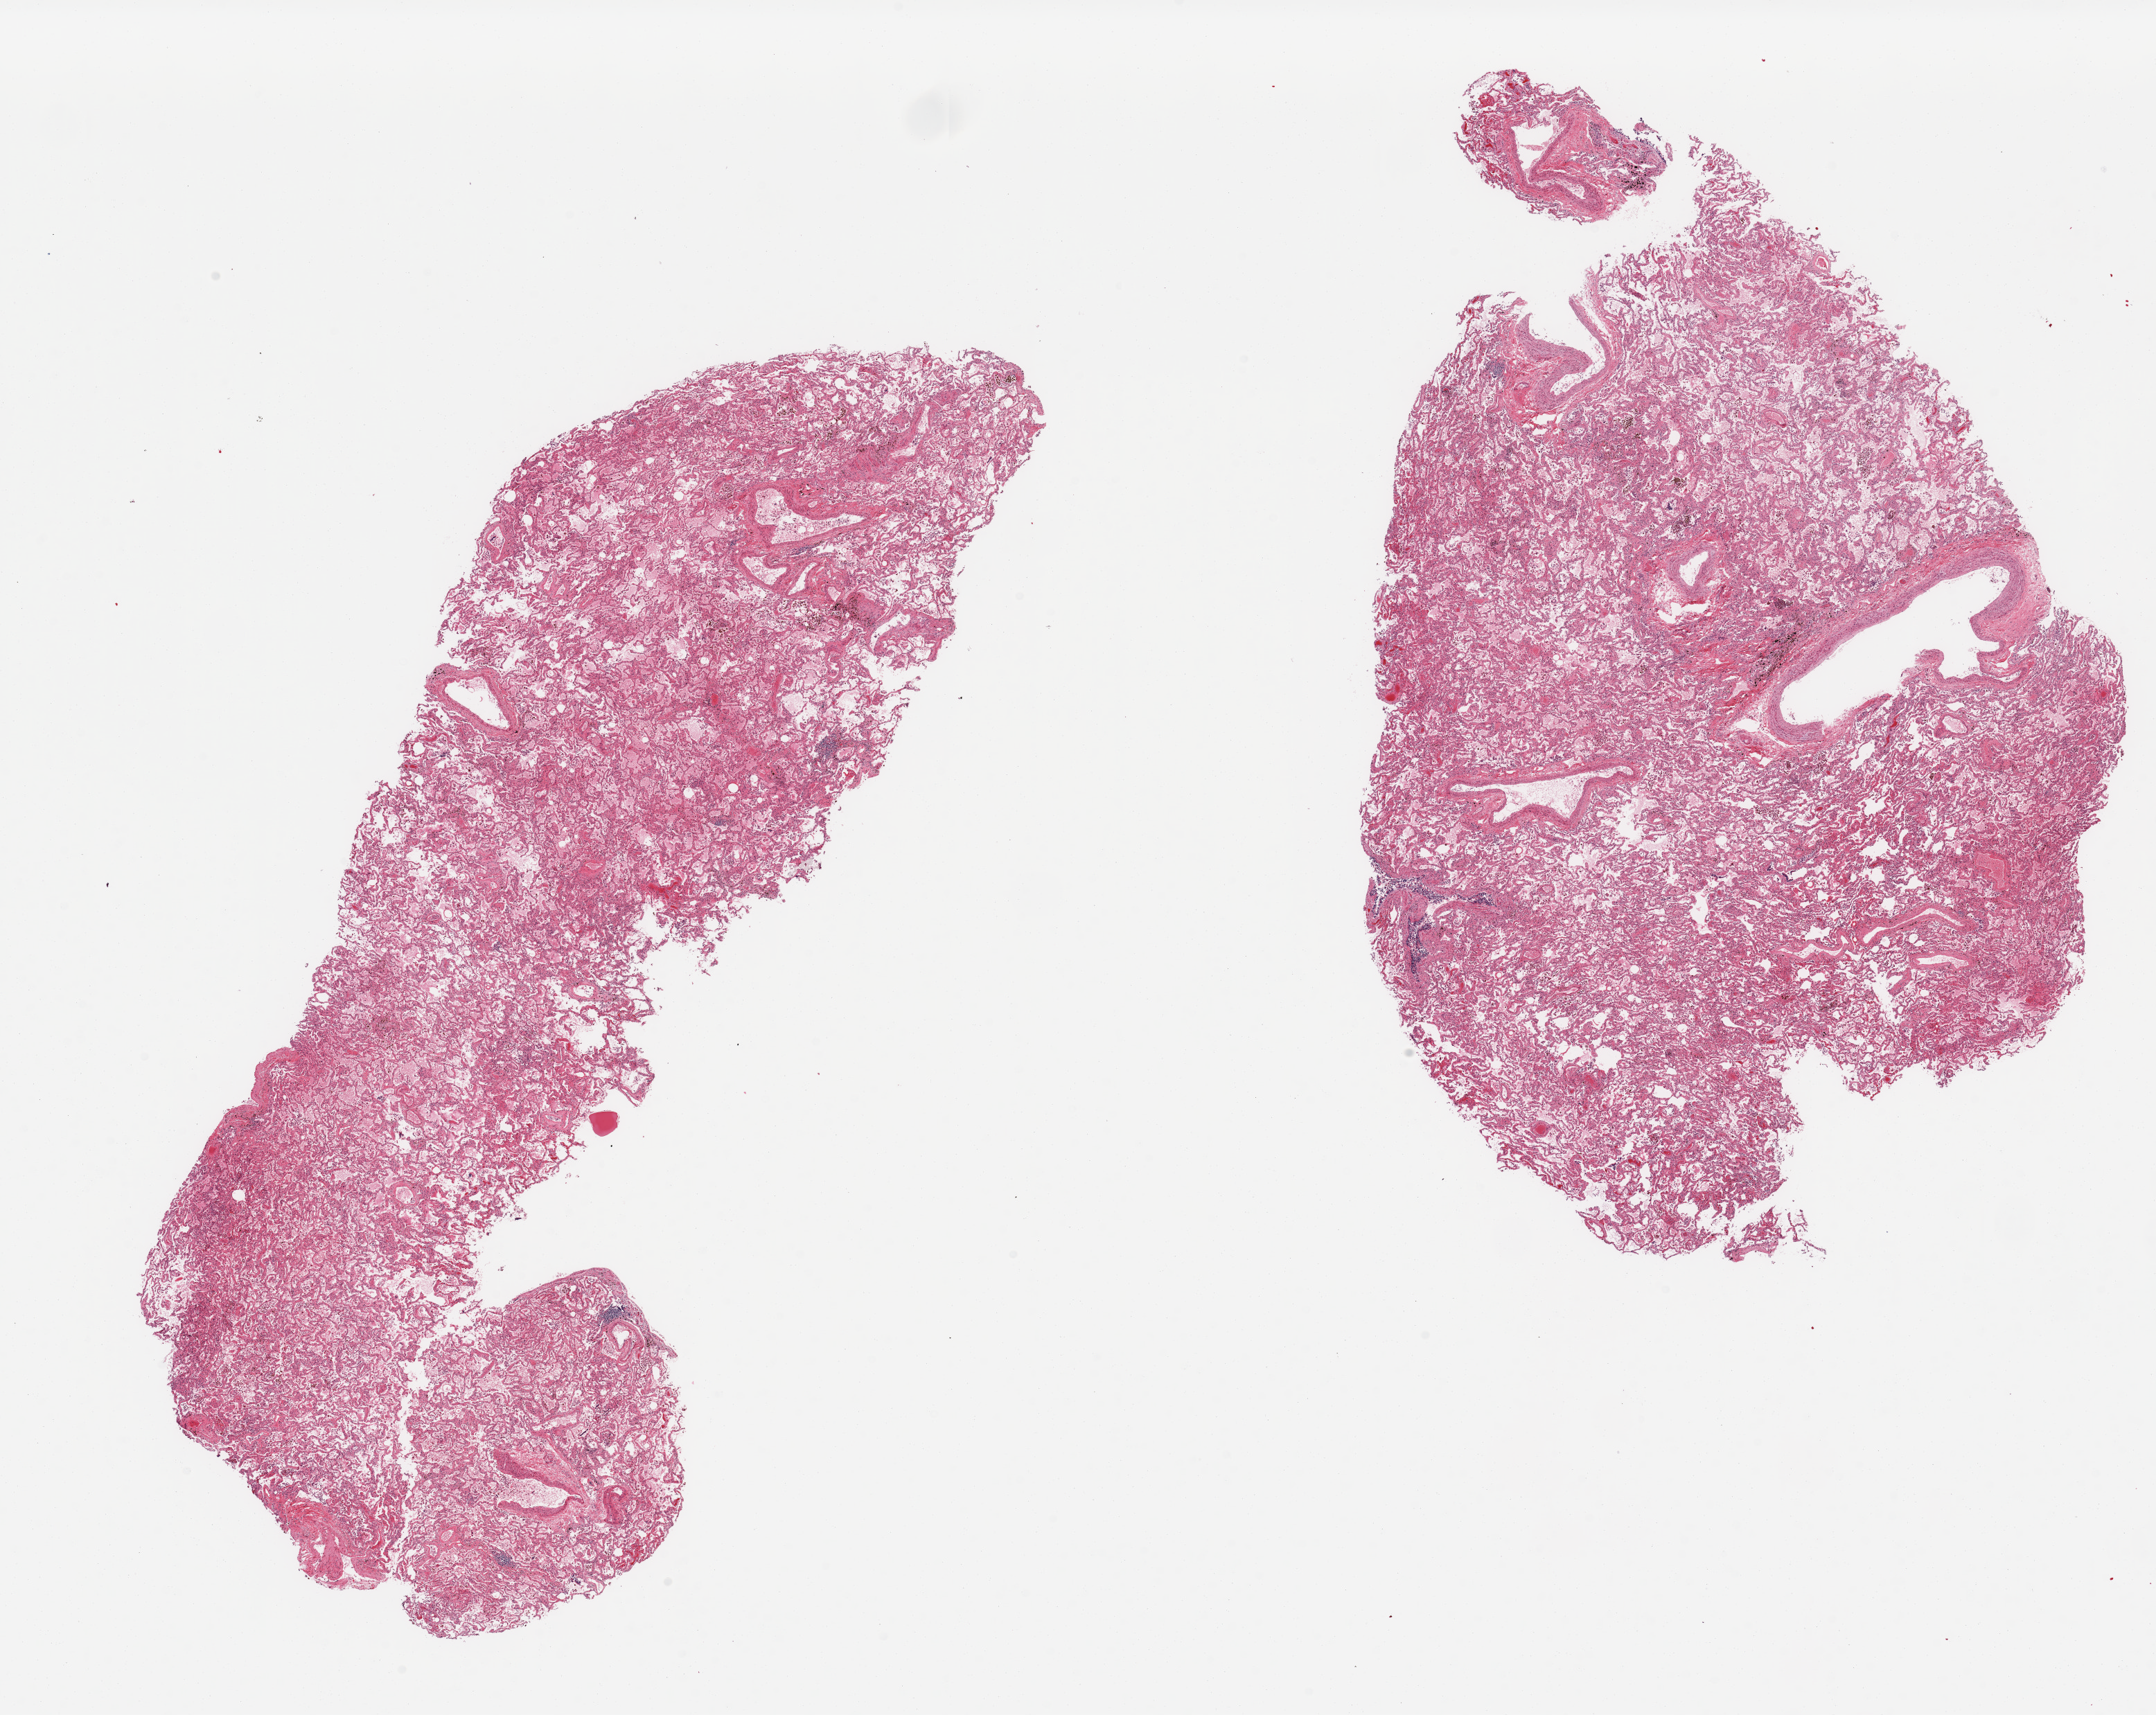
Hematoxylin and eosin (H&E) whole-slide image, brightfield — whole scanned area (about 24.6 x 19.6 mm) shown as a low-resolution overview, PAXgene-fixed paraffin-embedded (PFPE) section, target tissue: lung, tissue donor sample. Male donor.
Review note (as recorded): 2 pieces, chronic congestive changes.